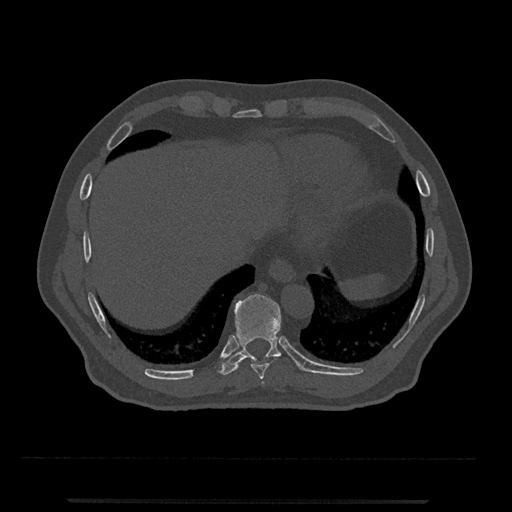
CT including the spine, one axial slice. Position 542 of 797 along the scan axis. Bone window (W 1800 / L 400 HU). 512 × 512 image matrix, field of view 419 × 419 mm. Patient: male, 63 years. From the clinical record (not read from this slice): primary cancer: prostate.
Annotated regions visible in this slice (semi-automatic segmentation, software-assisted and operator-edited):
- T10 vertebra: box from (x=218, y=294) to (x=282, y=375) px
- T8 vertebra: (x=262, y=382)–(x=264, y=384)
- T9 vertebra: (x=251, y=357)–(x=276, y=380)